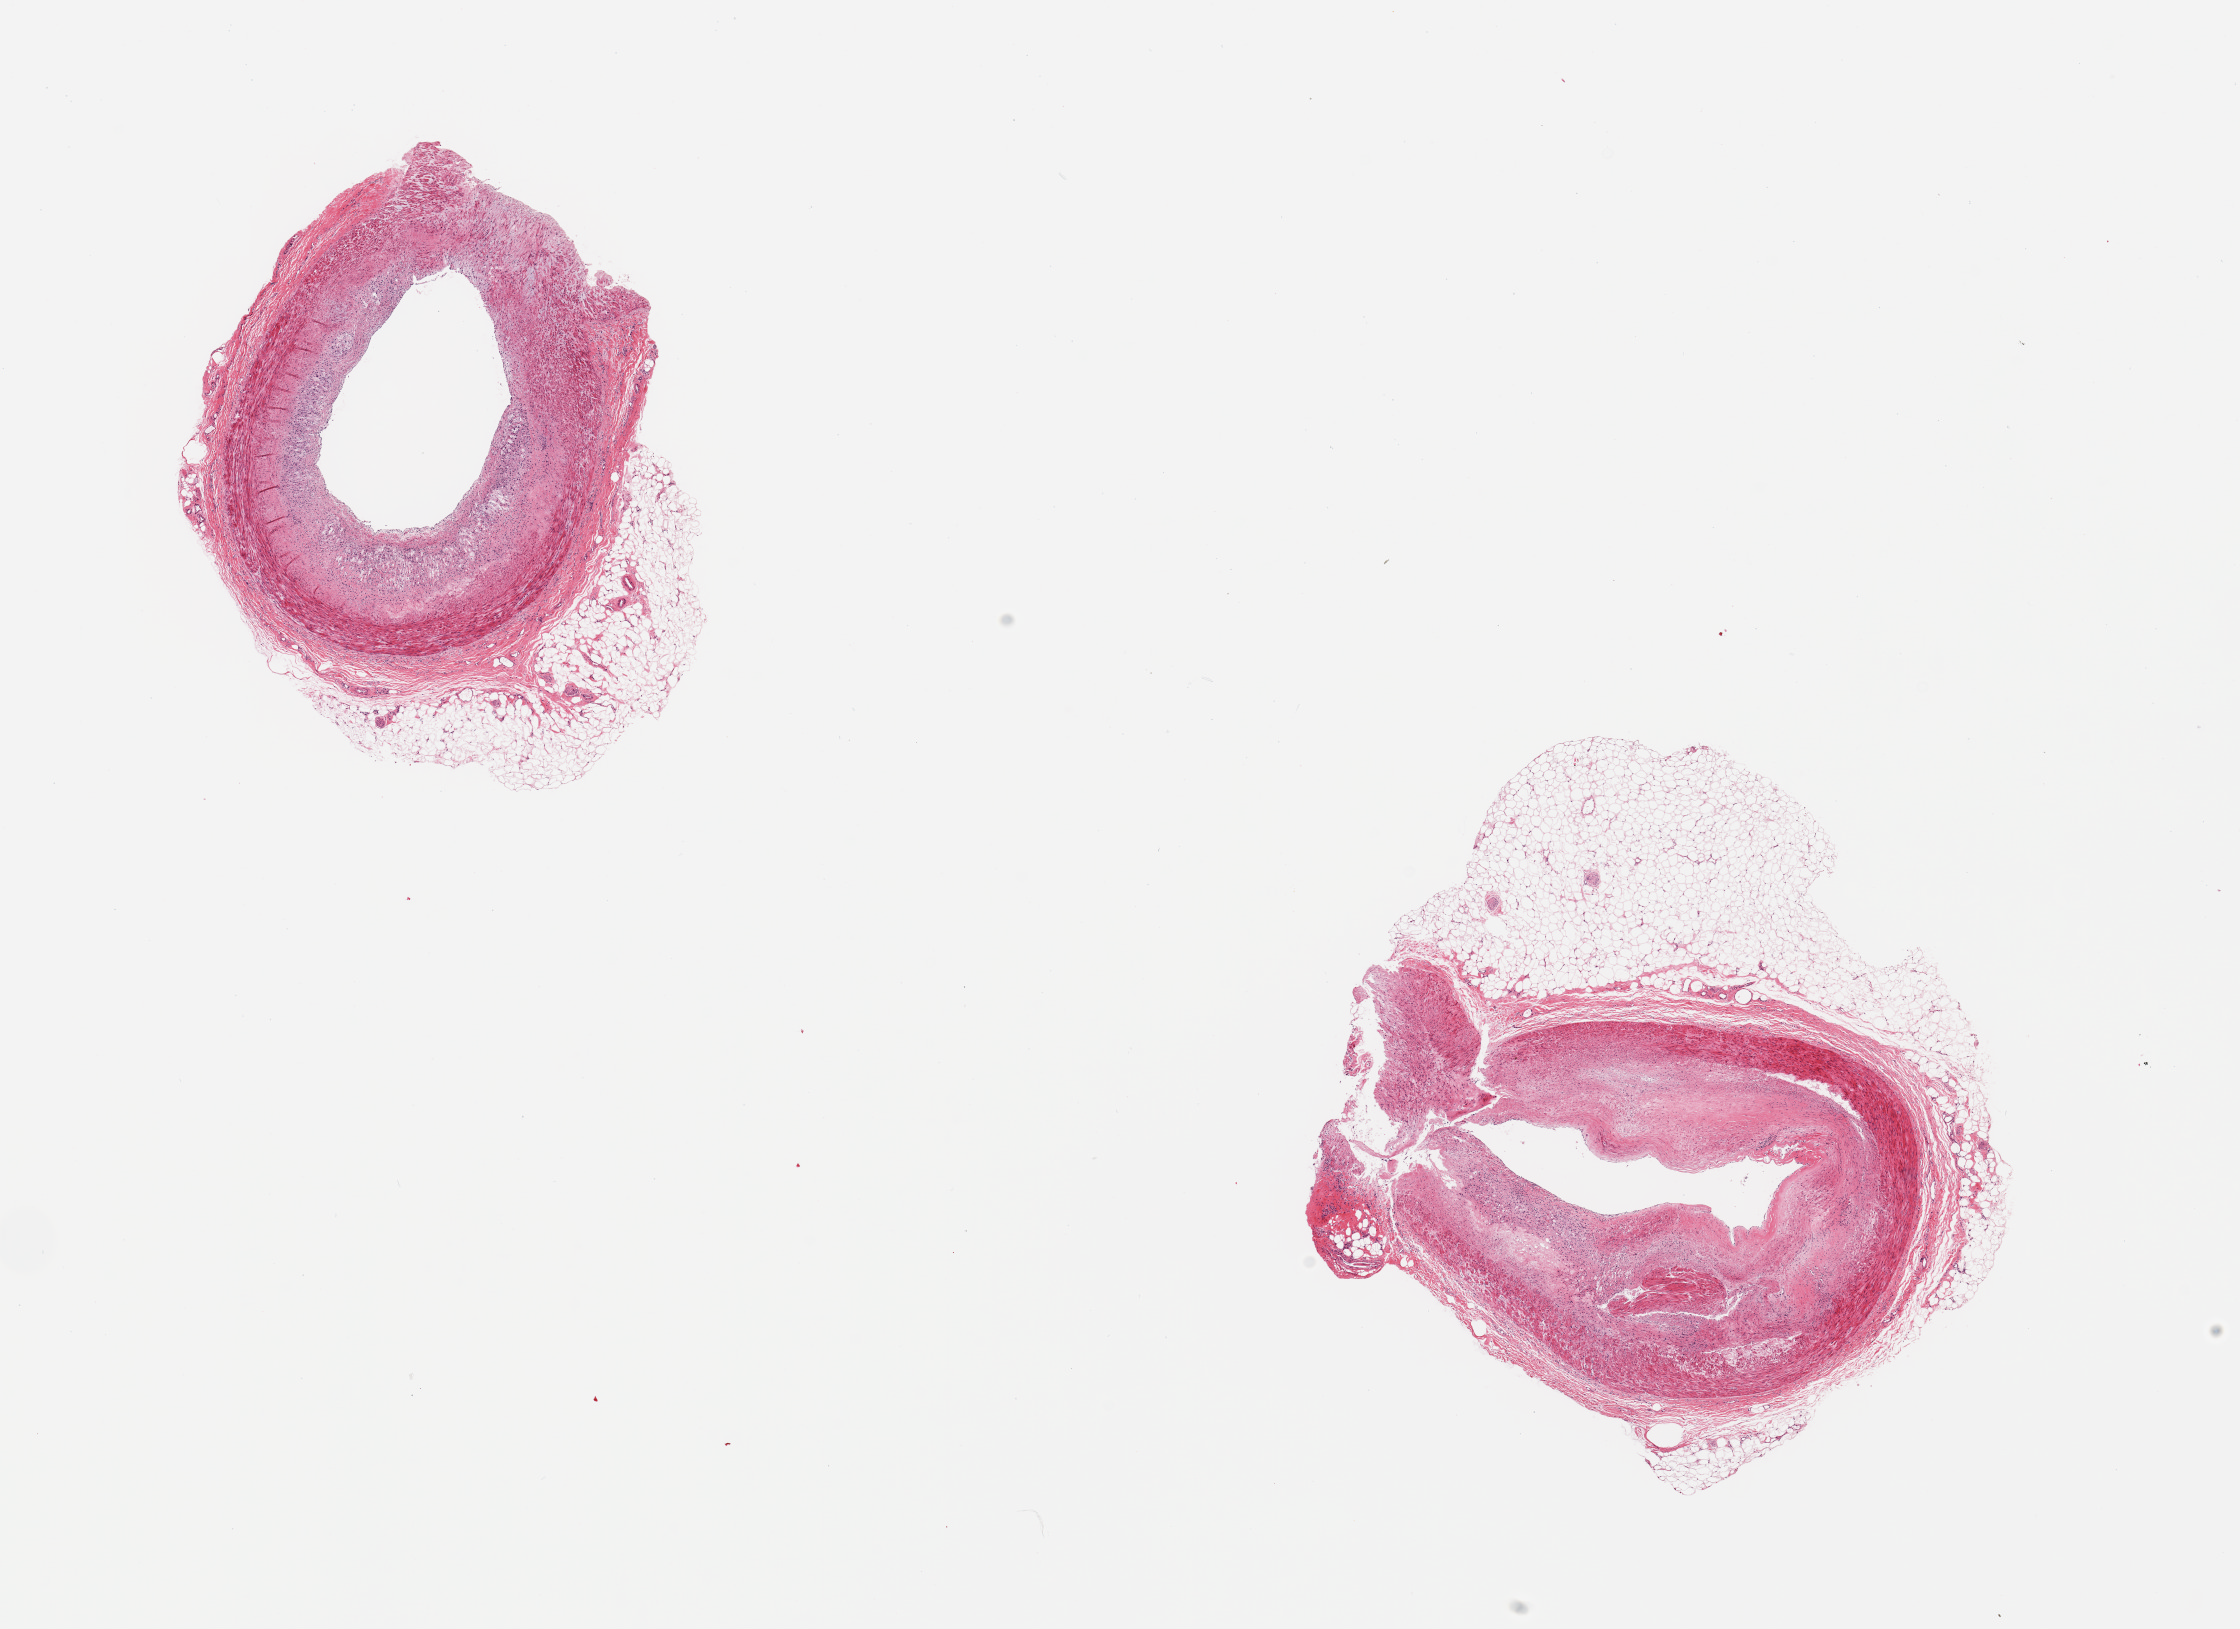
Hematoxylin and eosin (H&E) whole-slide image — shown as a low-resolution overview of the whole scanned area (about 17.7 x 12.9 mm, from a 20x scan); PAXgene-fixed, paraffin-embedded tissue; target tissue: coronary artery; tissue donor sample.
Pathologist's review note for this sample: 2 pieces; moderate plaques; external fat up to 2mm thick.